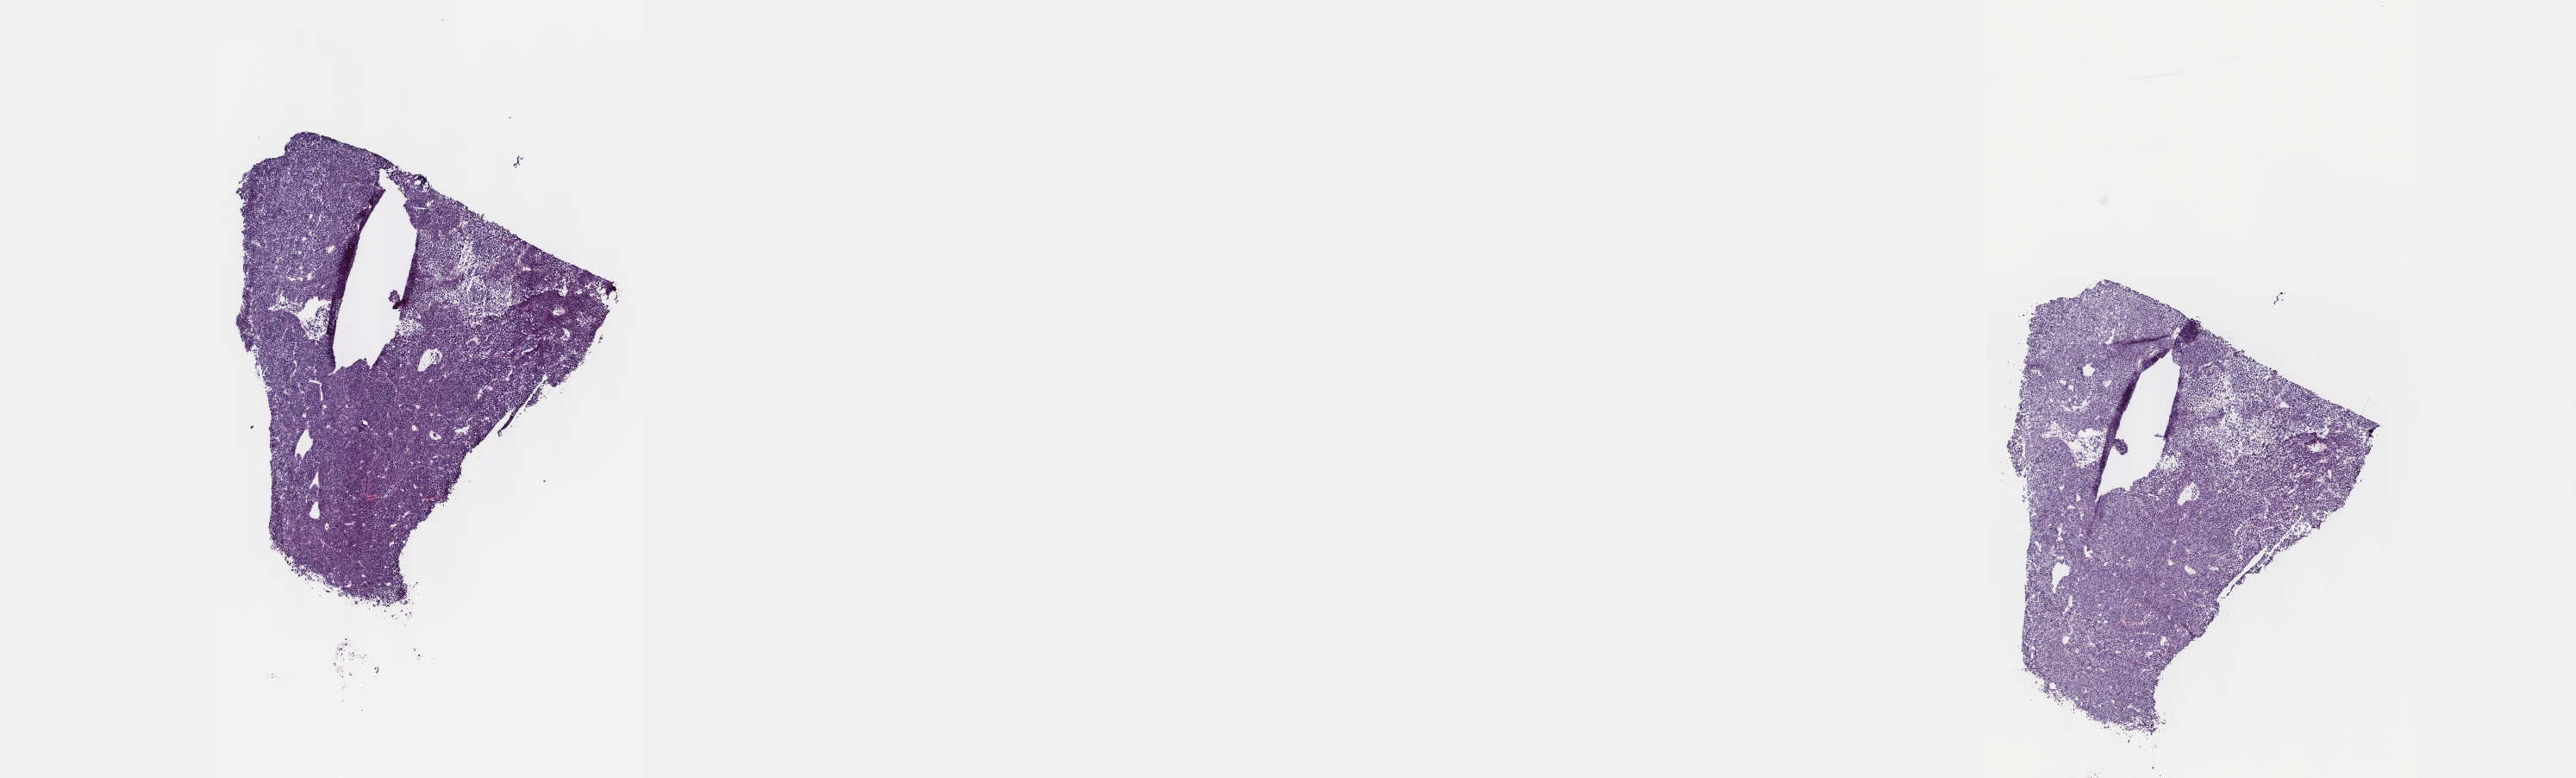
H&E-stained whole-slide image, whole scanned area (about 24.1 x 7.3 mm, slide scanned at 40x) shown as a low-resolution overview. Frozen section. Primary tumour sample from the uvea. Patient: male, age at initial diagnosis 60 years.
Histologic diagnosis: Epithelioid cell melanoma (choroid).